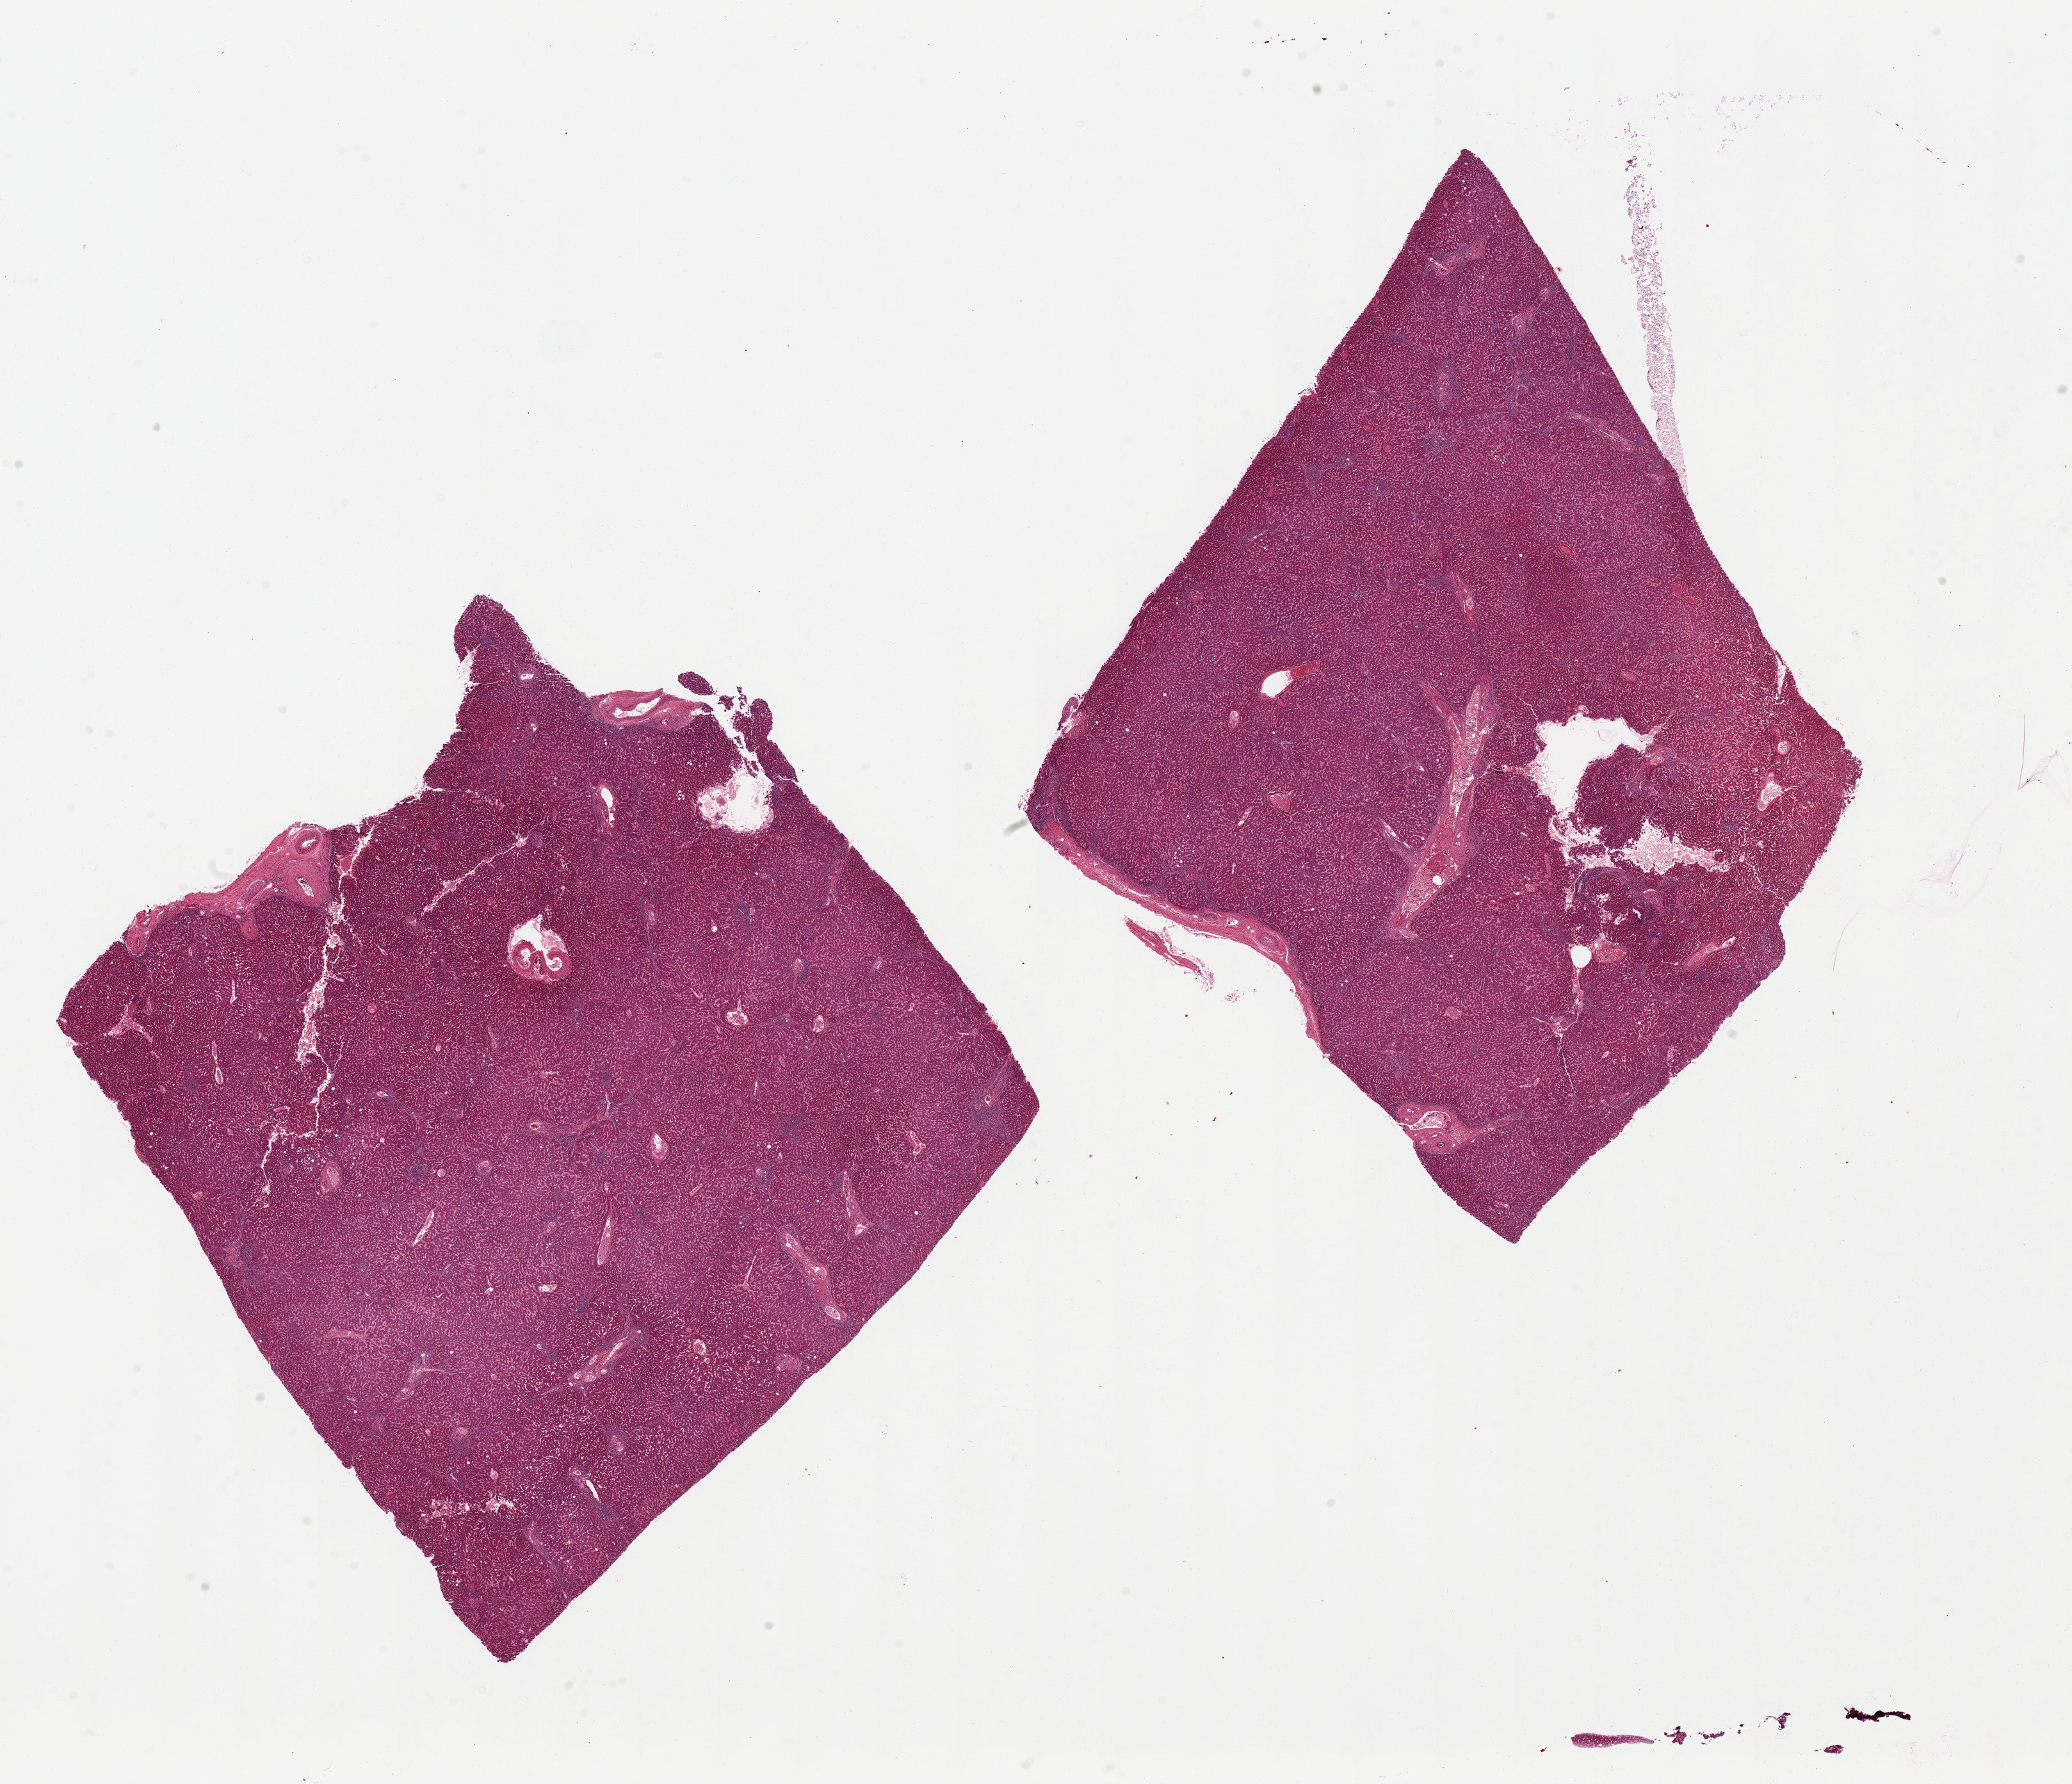
Whole-slide image, haematoxylin and eosin stain — whole scanned area (about 25.6 x 22.0 mm) shown as a low-resolution overview, PAXgene-fixed paraffin-embedded (PFPE) section, target tissue: liver, donor tissue sample. Female donor.
Reviewer comment on this tissue sample: 2 pieces, 11x10 & 10x9mm. Moderate portal lymphoid infiltrates consistent with chronic hepatitis or chronic biliary tract disease. No steatosis.